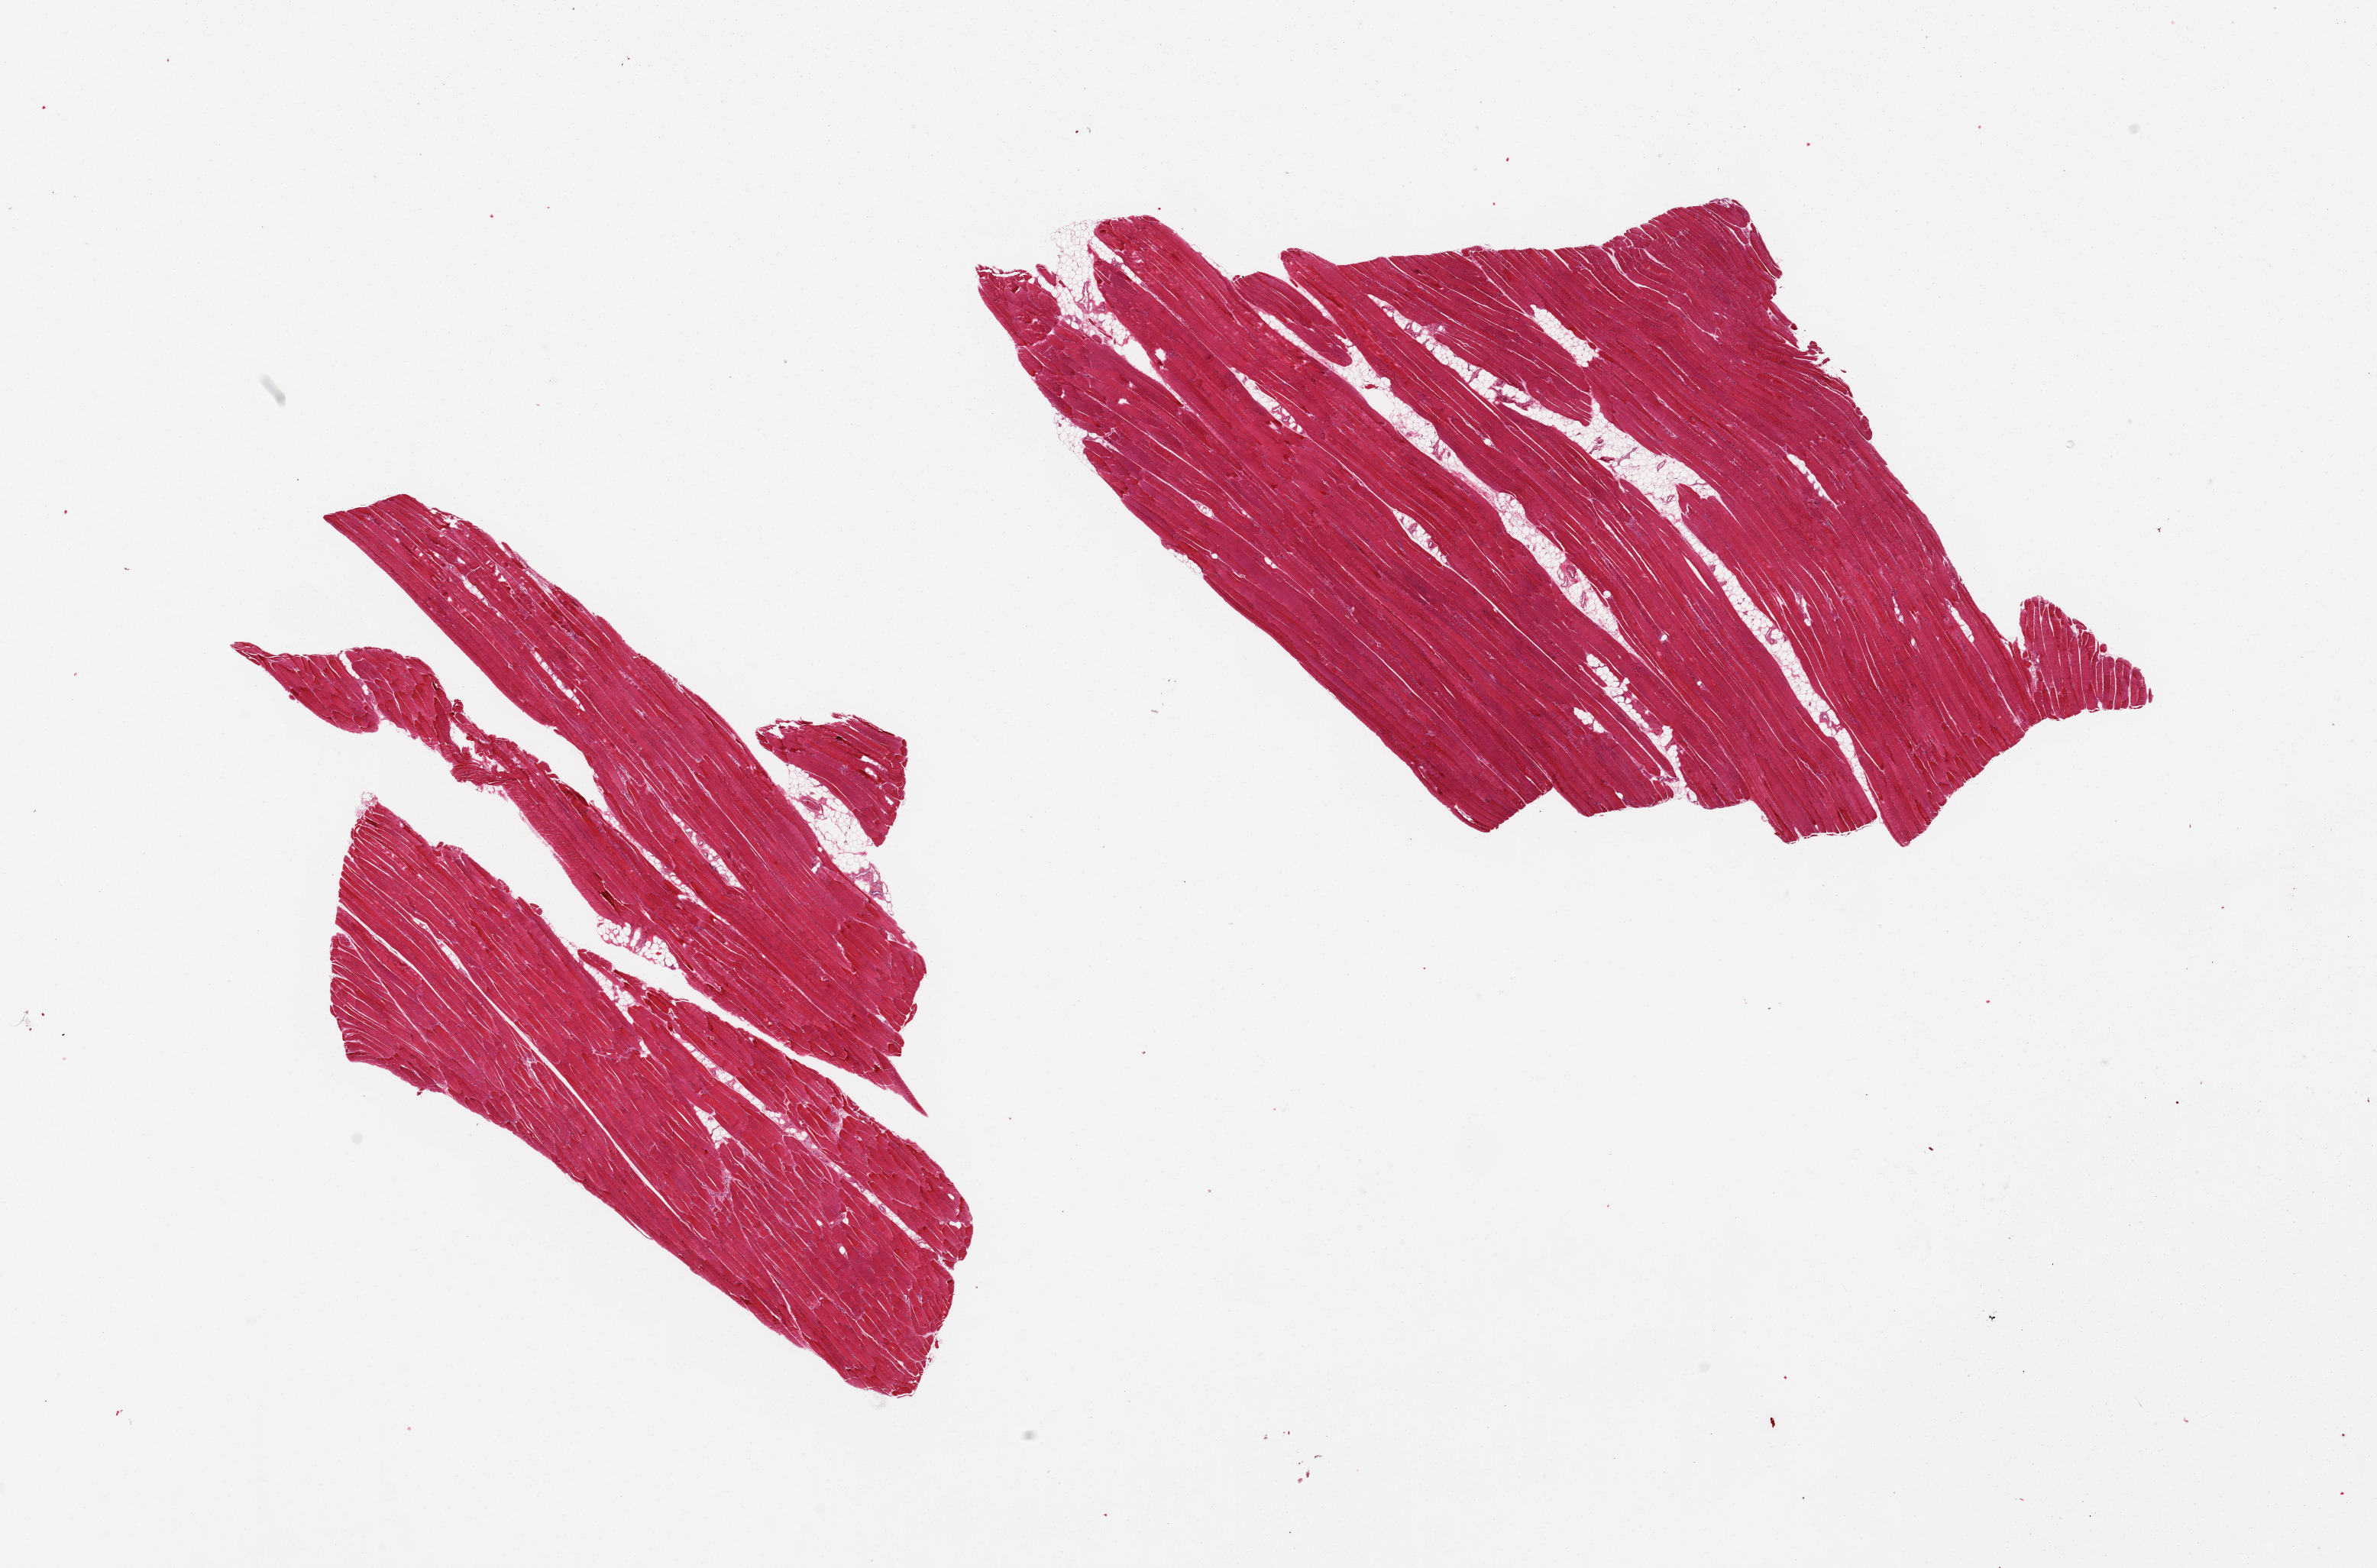
Hematoxylin and eosin (H&E) whole-slide image, brightfield — whole scanned area (about 24.6 x 16.2 mm, acquisition: 20x scan) shown as a low-resolution overview, PAXgene-fixed paraffin-embedded (PFPE) section, target tissue: skeletal muscle, donor tissue sample. Donor sex: female.
- reviewer comment on this tissue sample: 2 pieces, ~10% interstitial fat